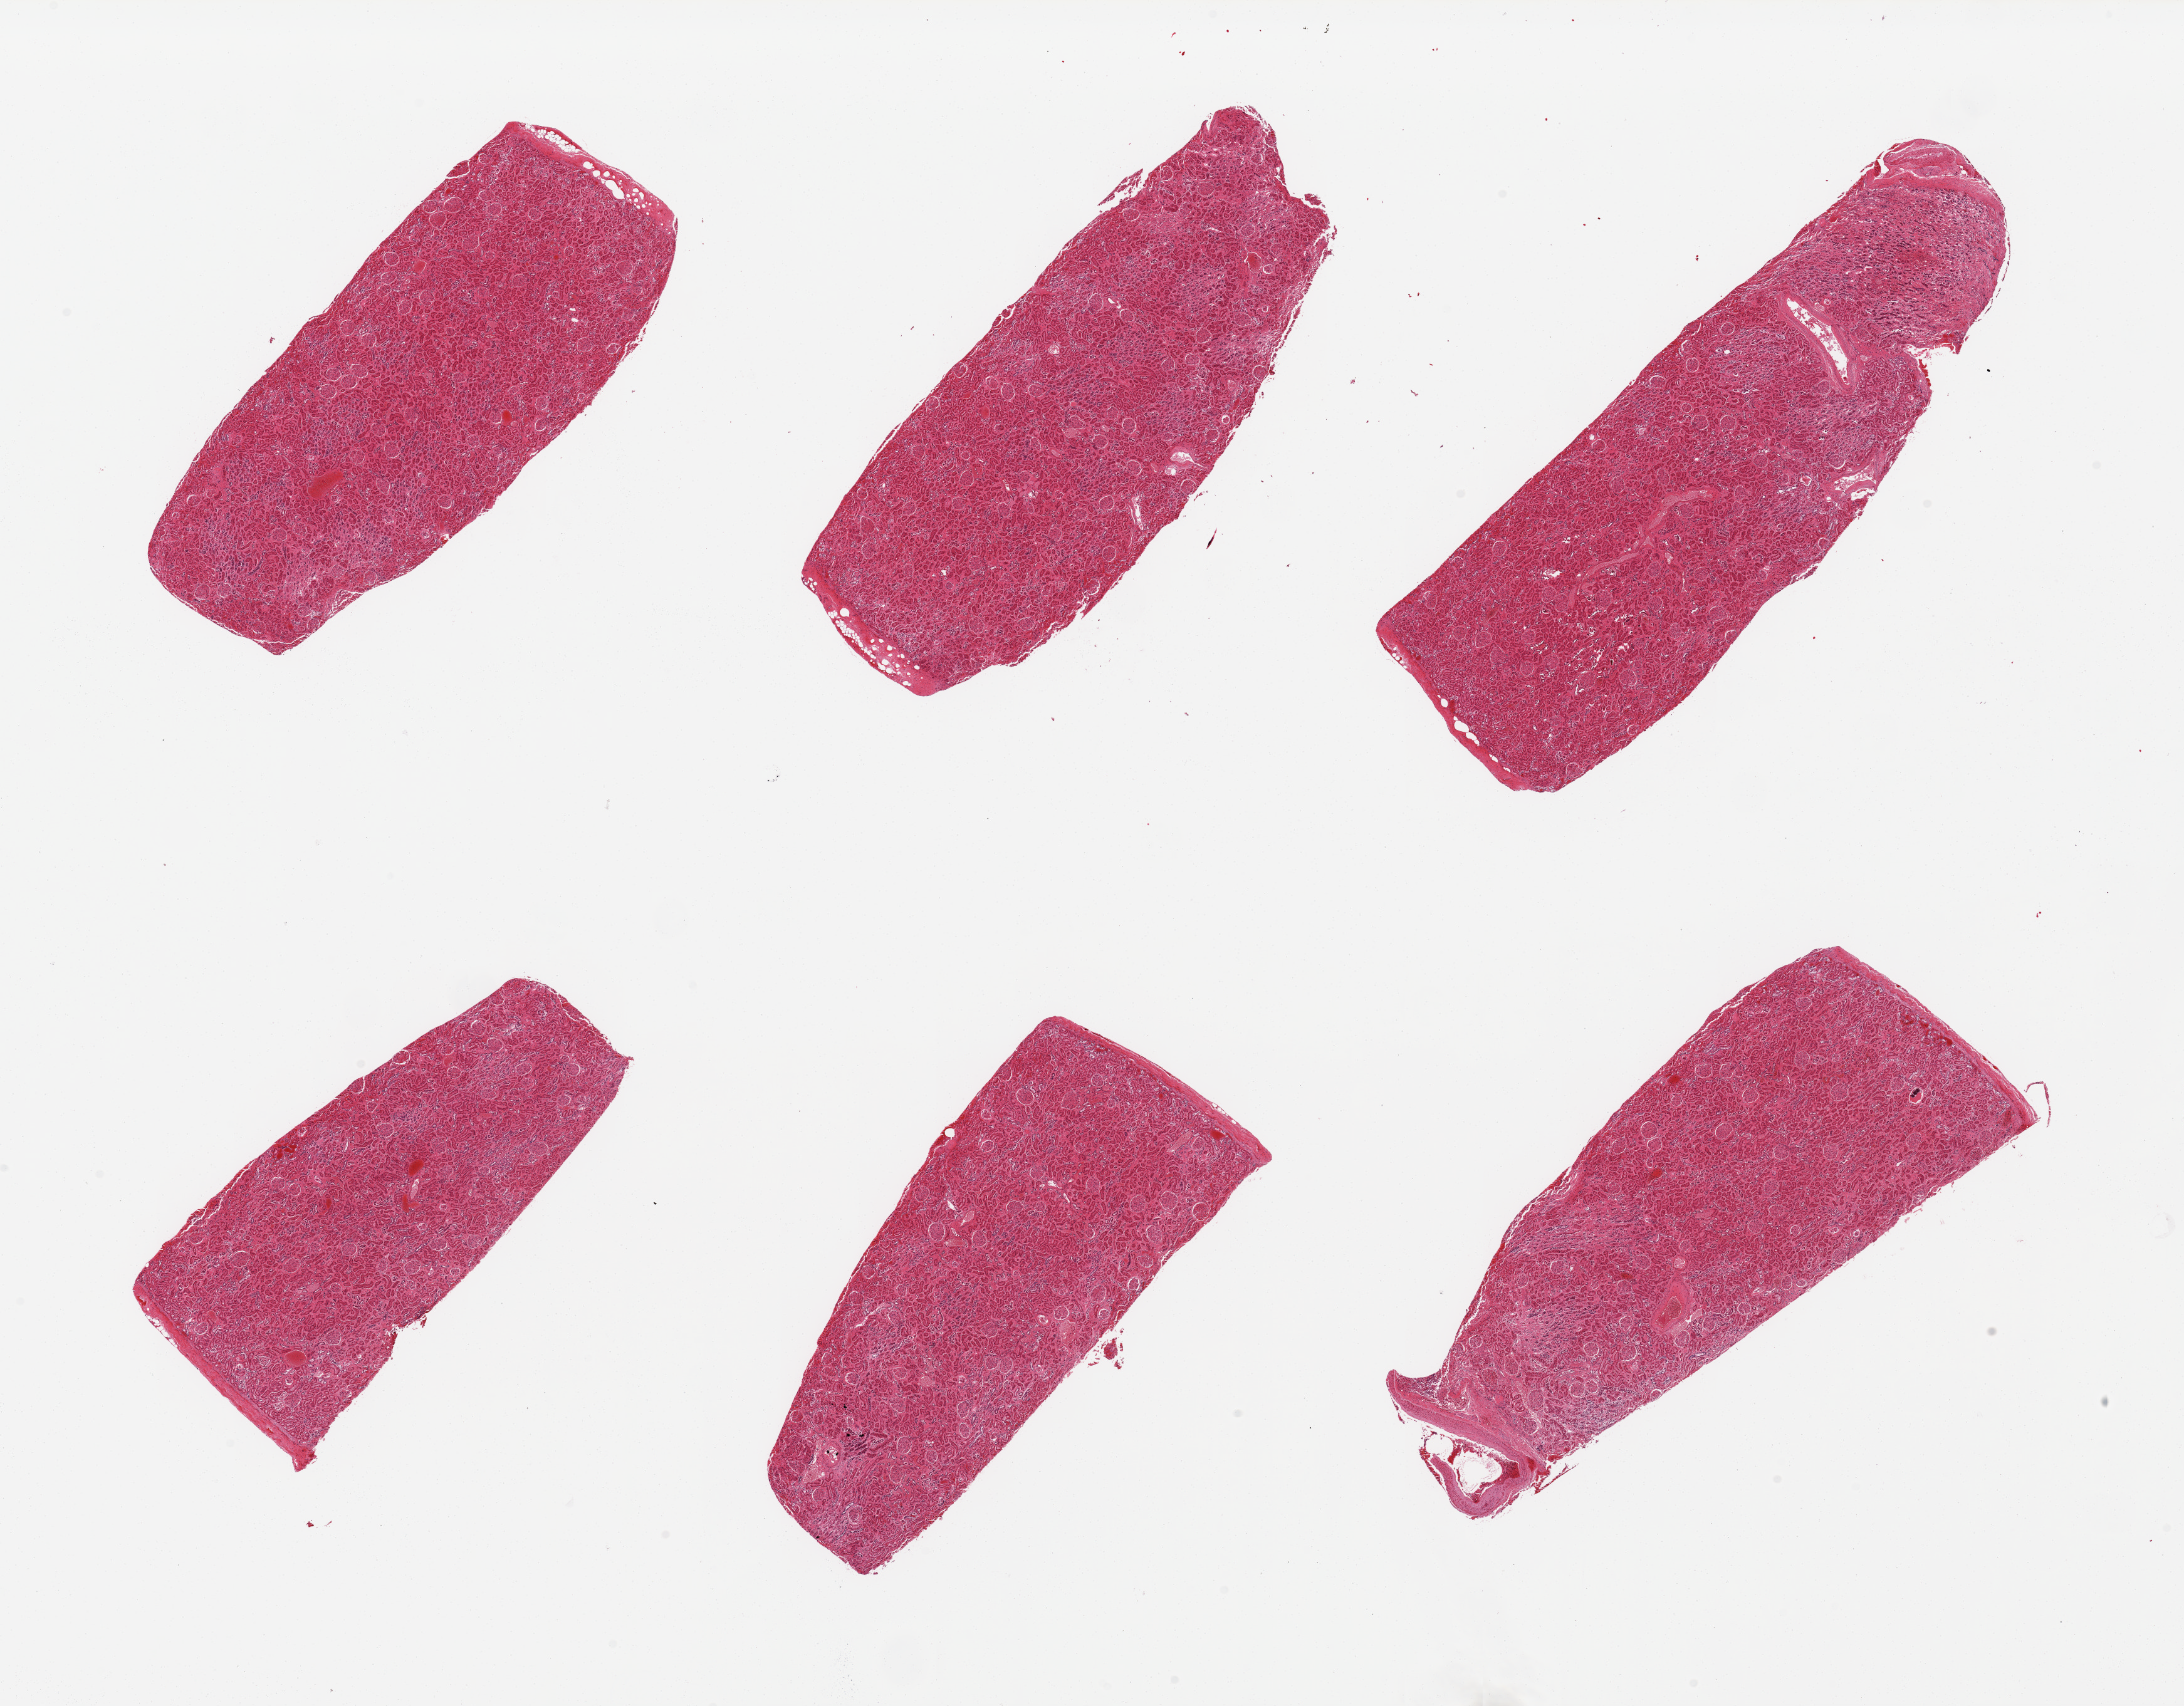
Digitized hematoxylin and eosin (H&E)-stained section, whole scanned area (about 27.6 x 21.5 mm, from a 20x scan) shown as a low-resolution overview; PAXgene-fixed paraffin-embedded (PFPE) section; sampled site (target tissue): renal cortex; donor tissue sample.
Reviewer comment on this tissue sample: 6 pieces, glomeruli present all sections; tubules moderate/severe autolysis.